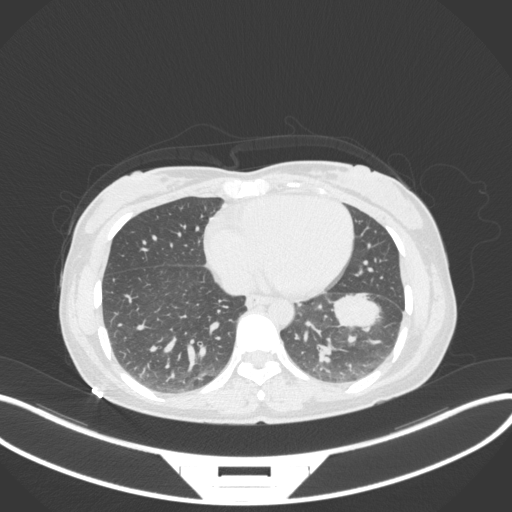
Chest CT, one axial slice; position 128 of 361 along the scan axis; lung window (W 1500 / L -600 HU); 1 mm slice thickness; 512 × 512 image matrix, field of view 400 × 400 mm. Patient: female, 41 years. From the clinical record (not read from this slice): clinical TNM (as recorded): T2a N3 M1b.
Annotated regions visible in this slice (bounding box drawn by a radiologist):
- lung tumour (recorded histology: adenocarcinoma): box from (x=330, y=289) to (x=389, y=338) px